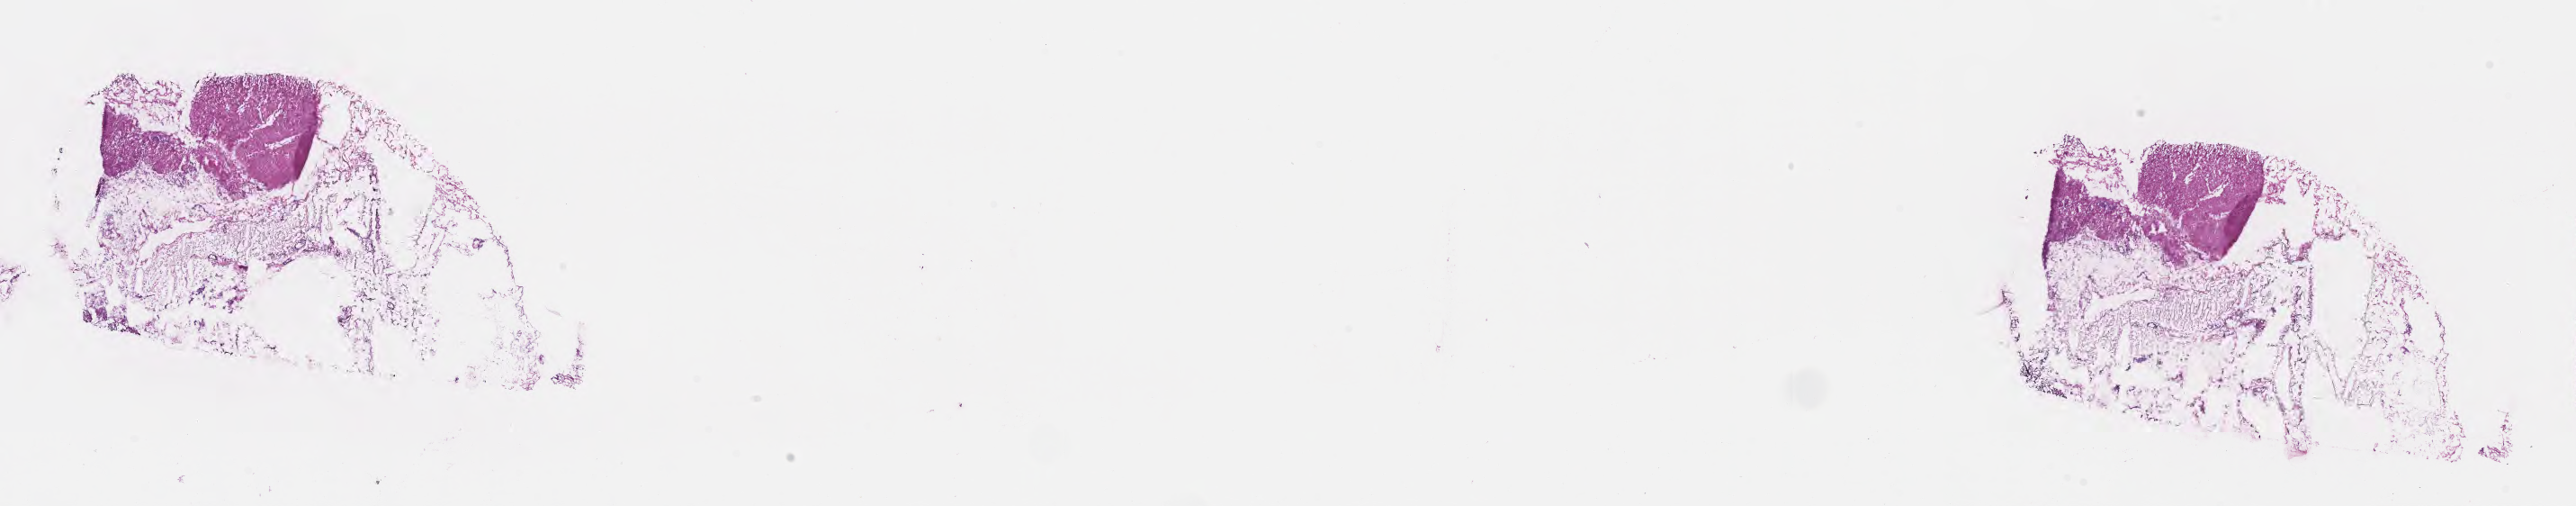
Hematoxylin and eosin (H&E) whole-slide image — whole scanned area (about 23.1 x 4.5 mm) shown as a low-resolution overview; frozen section; non-tumor (normal tissue) sample from a patient with adenocarcinoma, NOS; anatomic site: sigmoid colon. Male patient; age at initial diagnosis 82 years. Composition of this section per pathologist review: tumor cells 0%, tumor nuclei 0%, stromal cells 0%, necrosis 0%, normal cells 100%. Infiltration values recorded for this section: lymphocyte infiltration 0%, monocyte infiltration 0%, neutrophil infiltration 0%.
This section: non-tumor tissue sample; the patient's diagnosis is given above.